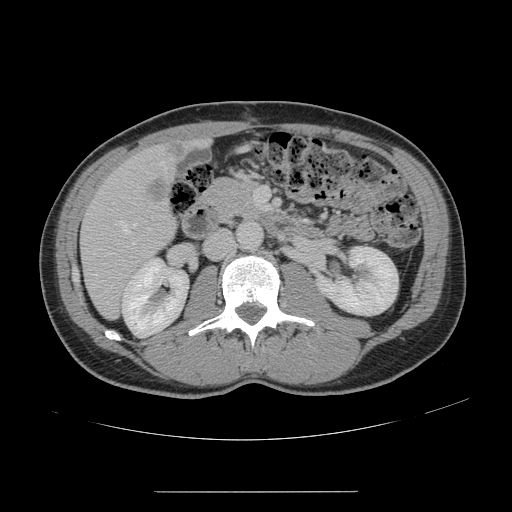
Contrast-enhanced abdominal CT, one axial slice; position 60 of 178 along the scan axis; 120 kVp; intravenous contrast given; soft-tissue window (W 400 / L 40 HU); 2.5 mm slice thickness; 512 × 512 image matrix, field of view 401 × 401 mm. Male patient, age 53 years. From the clinical record (not read from this slice): diagnosis: colorectal cancer liver metastases, imaged before liver resection; multiple liver metastases: yes; largest metastasis: 2.4 cm; chemotherapy before resection: yes.
Annotated regions visible in this slice (expert manual segmentation):
- hepatic veins: bounding box [x1, y1, x2, y2] px = [95, 161, 164, 276]
- liver: [82, 140, 199, 317]
- portal vein (with intrahepatic branches): [254, 187, 267, 210]
- liver metastasis: [169, 143, 187, 156]
- liver metastasis: [146, 179, 169, 203]